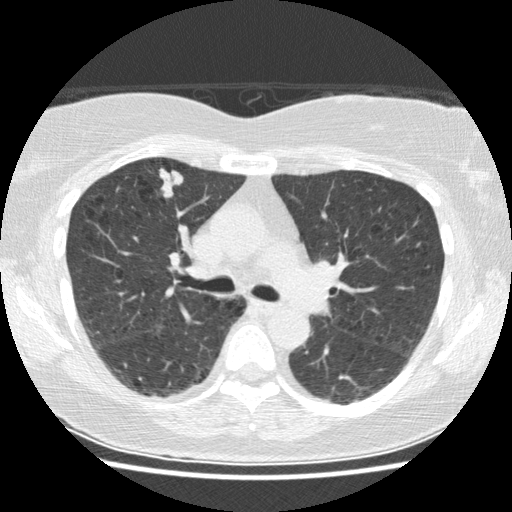
Axial slice from a low-dose chest CT screening exam; baseline screening round; lung window (W 1500 / L -600 HU); 2.5 mm slice thickness; standard (soft-tissue) reconstruction kernel (STANDARD); slice 61 of 155 in the series. Female participant, aged 63 years at enrolment.
Expert reader's lesion annotation, bounding box (x1, y1, x2, y2) in pixels: (145, 156, 188, 210). The exam's reader record, not a measurement of the box and not confirmed to be the same lesion: non-calcified nodule or mass ≥4 mm, right upper lobe, 18 × 14 mm, spiculated (stellate) margins, soft tissue attenuation. Official screen result: positive, change unspecified: nodule(s) >= 4 mm or enlarging nodule(s), mass(es), or other non-specific abnormalities suspicious for lung cancer. Lung cancer was diagnosed 87 days after this screen: papillary adenocarcinoma, NOS, right upper lobe, well differentiated (G1), stage IA (AJCC 6th edition), 19 mm at pathology.